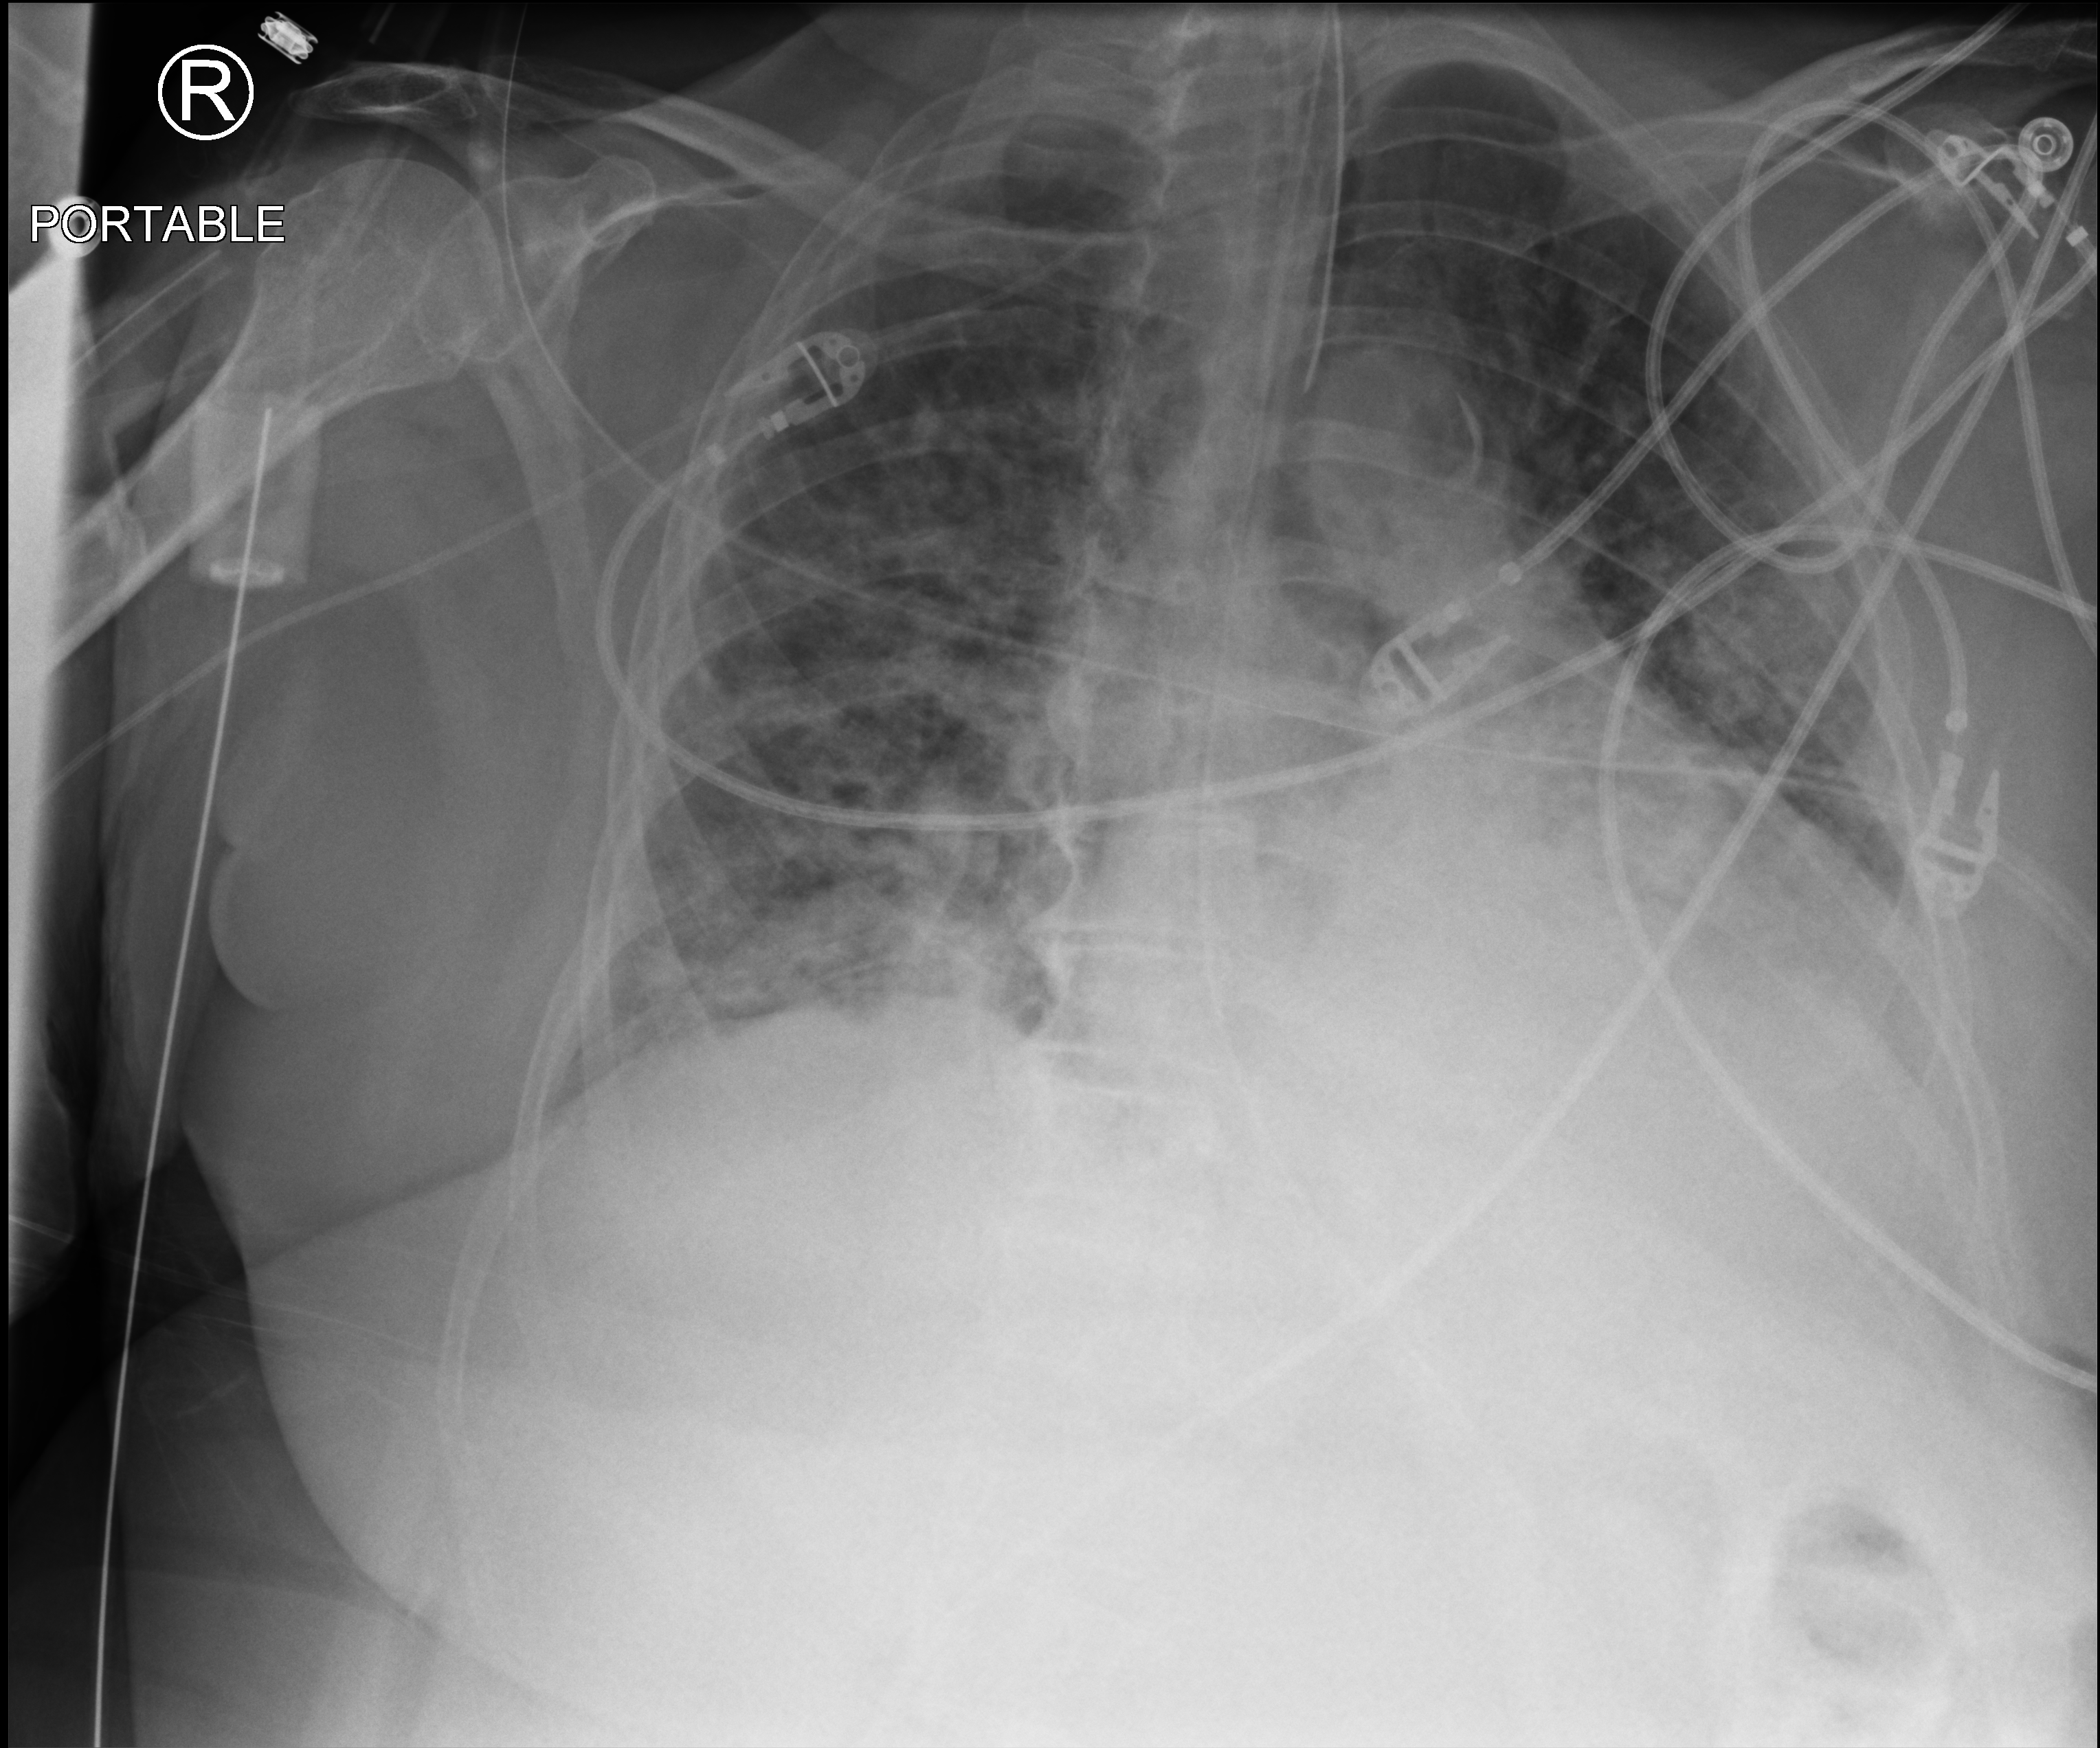
Bedside chest radiograph (computed radiography). Female patient hospitalised with COVID-19, age 75–90 years.
Admission-level facts for this patient (not findings on this image; timing relative to this image not recorded):
- other chronic lung disease (admission record): yes
- mechanically ventilated during this hospital stay: yes